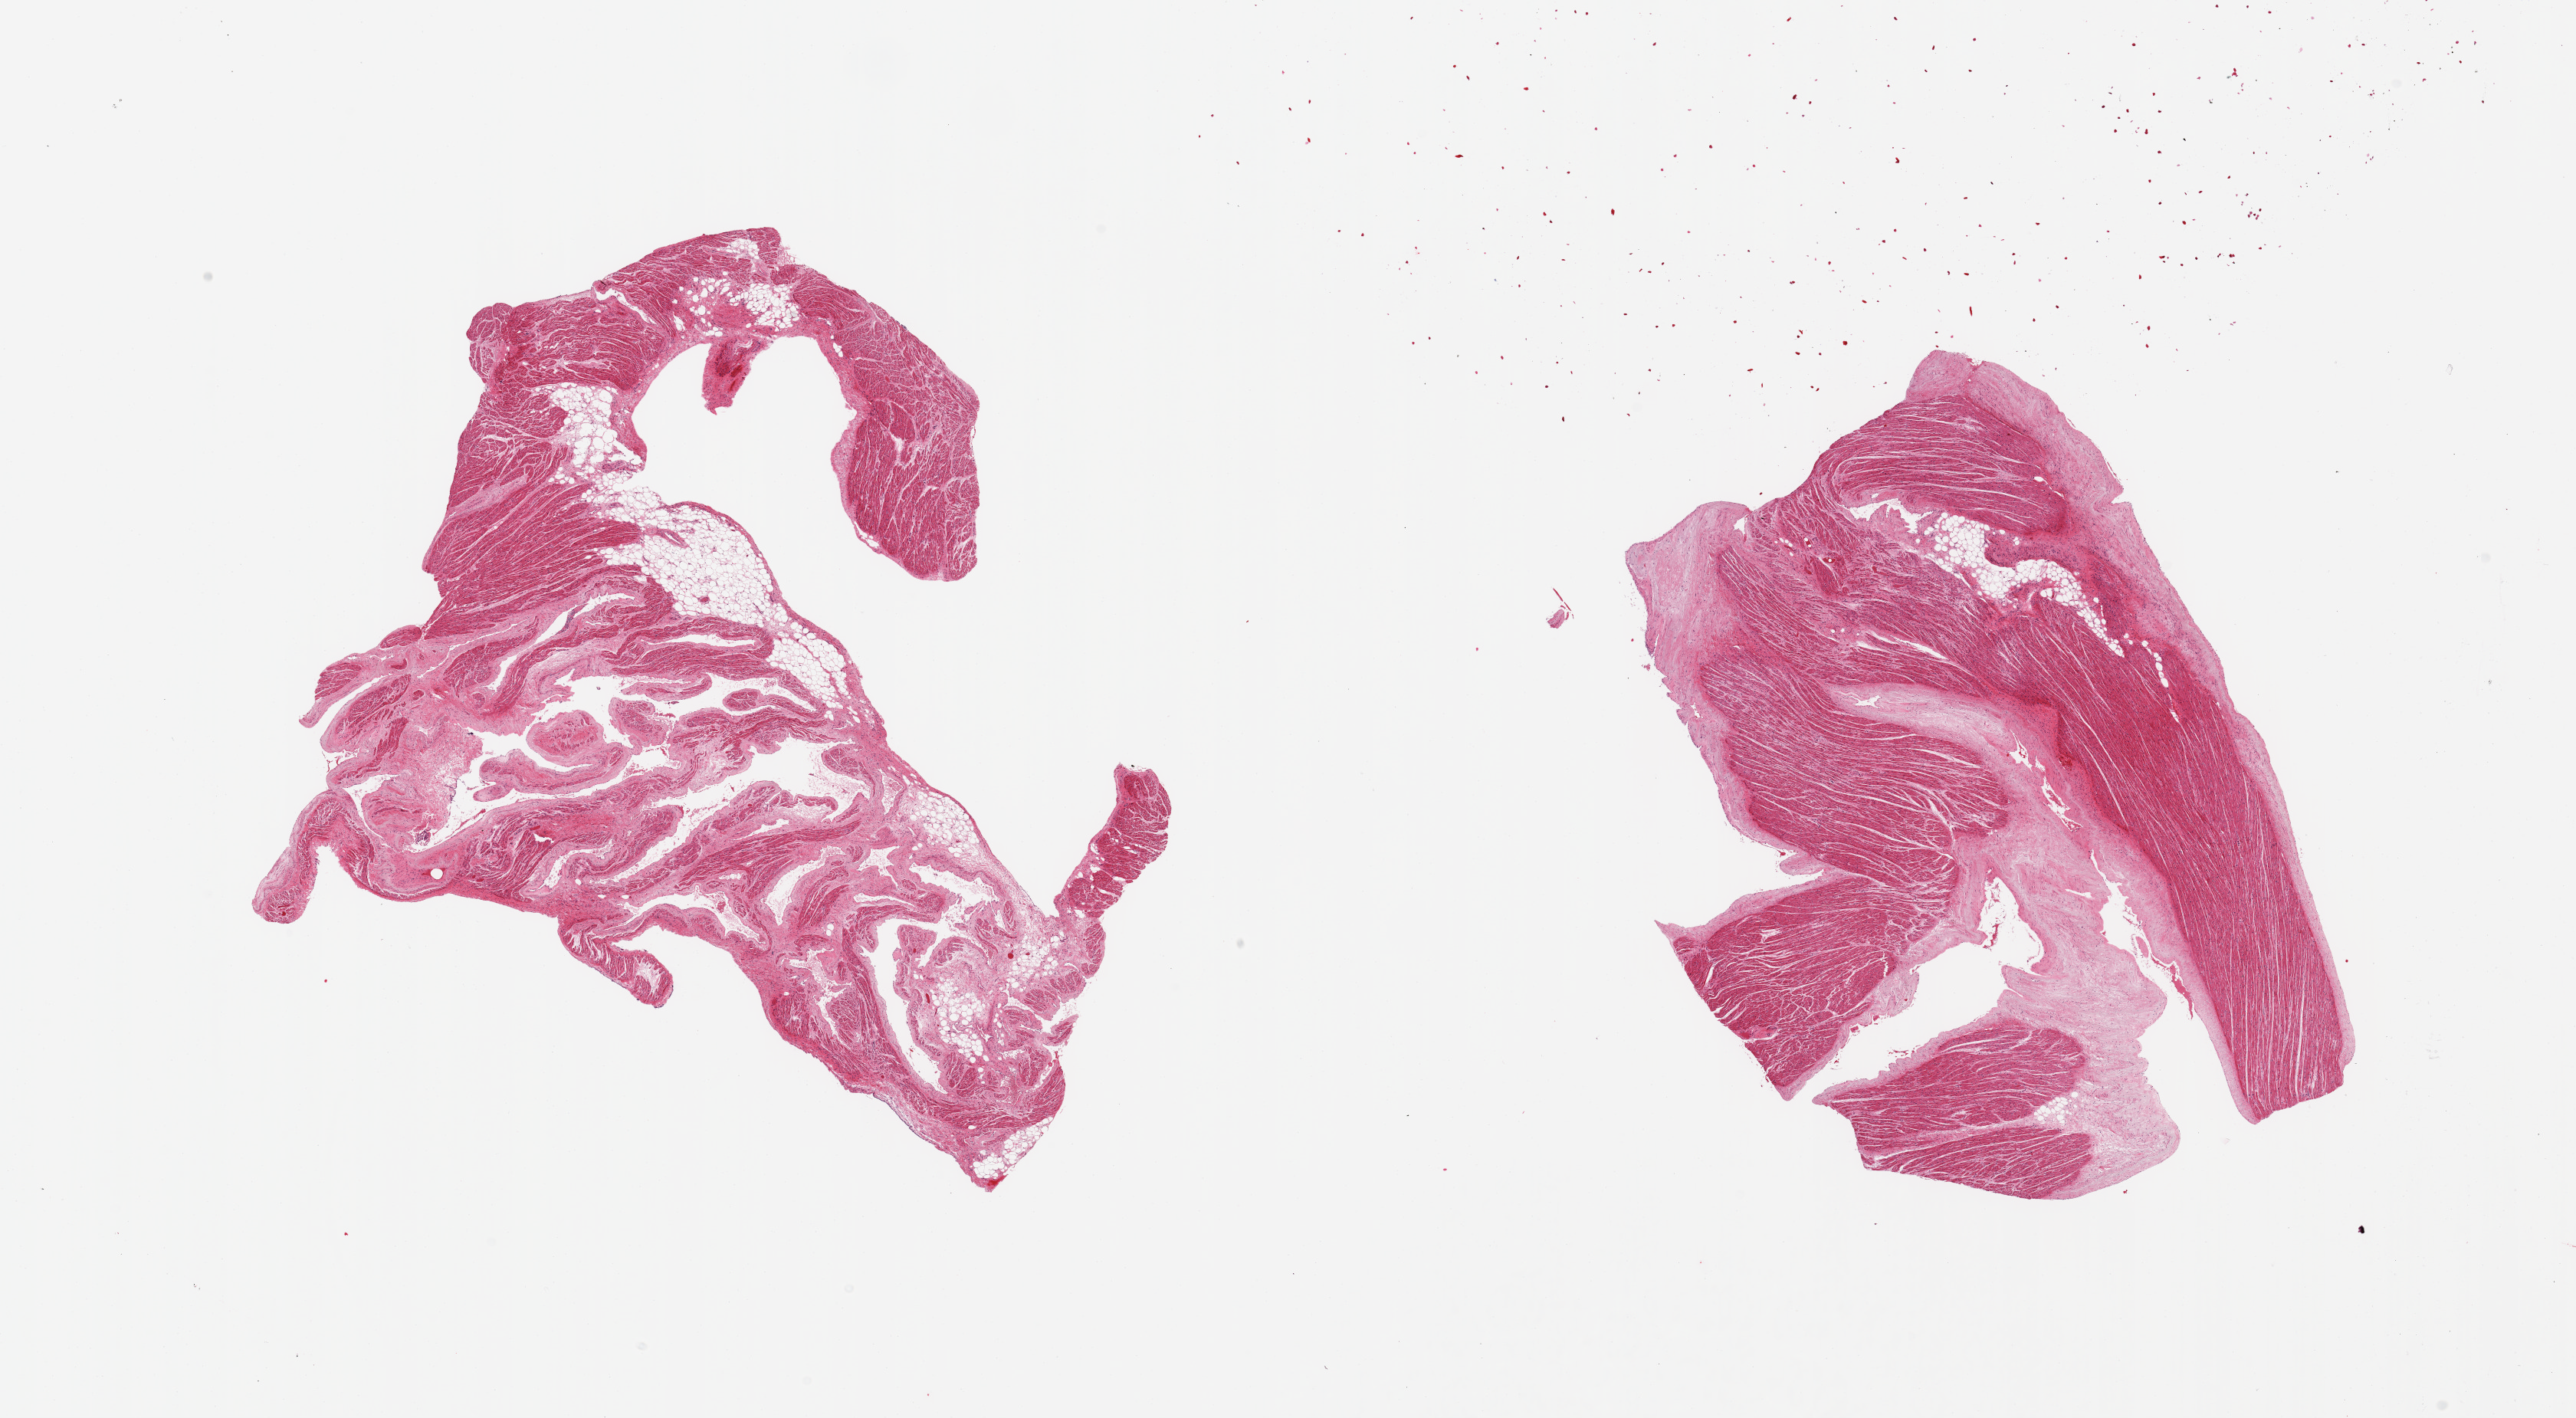
H&E whole-slide image, a low-resolution overview of the entire scanned area, about 26.6 x 14.6 mm. PAXgene-fixed, paraffin-embedded tissue. Section of auricular appendage (target tissue). Donor tissue sample. Female donor.
- review note (as recorded): 2 pieces; 20% internal fibrofatty content